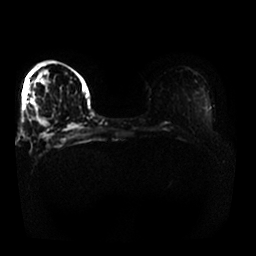
Breast MRI, one axial slice. Slice 13 of 25 in the series (ordered by position). Diffusion-weighted series; image 2 of 4 stored at this slice position (different b-values; order by instance number). 1.5 T. 4 mm slice thickness. 256 × 256 image matrix. Female patient.
Outlined on this slice (expert manual segmentation):
- tumour on diffusion-weighted imaging: bounding box [x1, y1, x2, y2] px = [40, 79, 49, 127]